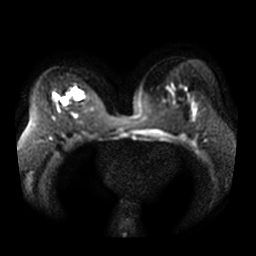
Breast MRI, one axial slice. Diffusion-weighted series; image 2 of 4 stored at this slice position (different b-values; order by instance number). 3 T. 5 mm slice thickness. 256 × 256 image matrix, field of view 370 × 370 mm. Female patient.
Structures marked on this image (expert manual segmentation):
- tumour on diffusion-weighted imaging: box from (x=62, y=90) to (x=81, y=104) px